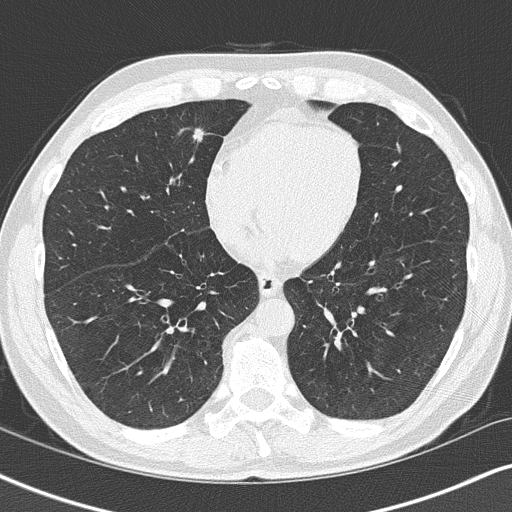
Low-dose screening chest CT, axial slice; second screening round (one year after baseline); lung window (W 1500 / L -600 HU); 2 mm slice thickness; lung (sharp) reconstruction kernel (B50f); slice 106 of 148 in the series. Male participant, aged 58 years at enrolment. Current smoker at enrolment.
Expert reader's lesion annotation, box from (x=168, y=111) to (x=223, y=157) px. The exam's reader record, not a measurement of the box and not confirmed to be the same lesion: non-calcified nodule or mass ≥4 mm, right middle lobe, 8 × 8 mm, spiculated (stellate) margins, soft tissue attenuation, pre-existing on the prior screen: yes; interval growth: yes. Official screen result: positive, other.